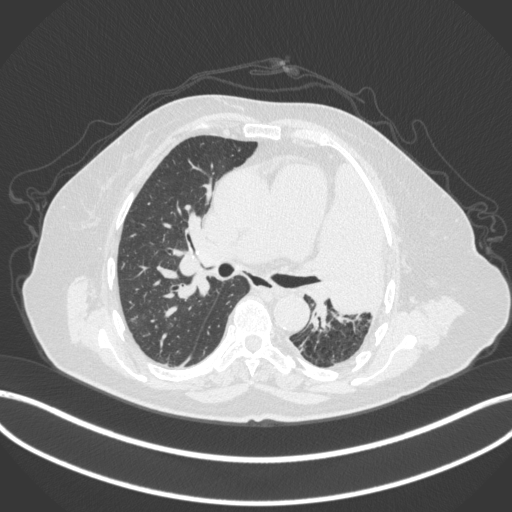
Chest CT, one axial slice; position 232 of 399 along the scan axis; lung window (W 1500 / L -600 HU); 1 mm slice thickness; 512 × 512 image matrix, field of view 400 × 400 mm. Patient: female, 75 years. From the clinical record (not read from this slice): clinical TNM (as recorded): T3 N3 M1.
Annotated regions visible in this slice (bounding box drawn by a radiologist):
- lung tumour (recorded histology: adenocarcinoma): box from (x=312, y=153) to (x=391, y=322) px